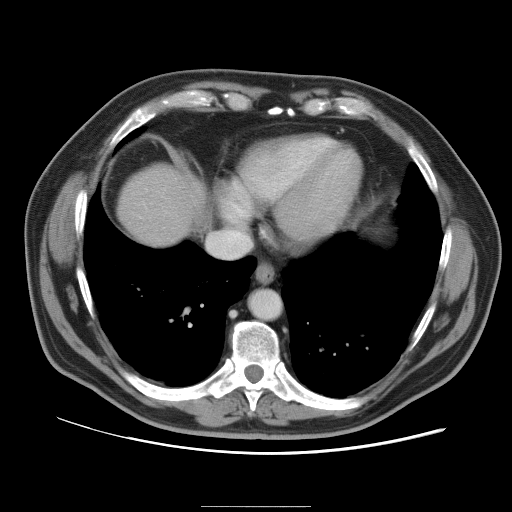
Contrast-enhanced abdominal CT, one axial slice. Slice 93 of 105 in the series (ordered by position). 120 kVp. Intravenous contrast given. Soft-tissue window (W 400 / L 40 HU). 5 mm slice thickness. 512 × 512 image matrix, field of view 399 × 399 mm. Male patient, age 64 years. From the clinical record (not read from this slice): diagnosis: colorectal cancer liver metastases, imaged before liver resection; multiple liver metastases: yes; largest metastasis: 3 cm.
Outlined on this slice (outlined manually by an expert reader):
- liver: bounding box [x1, y1, x2, y2] px = [118, 165, 201, 246]
- planned liver remnant (the part of the liver to remain after resection): [118, 167, 199, 245]